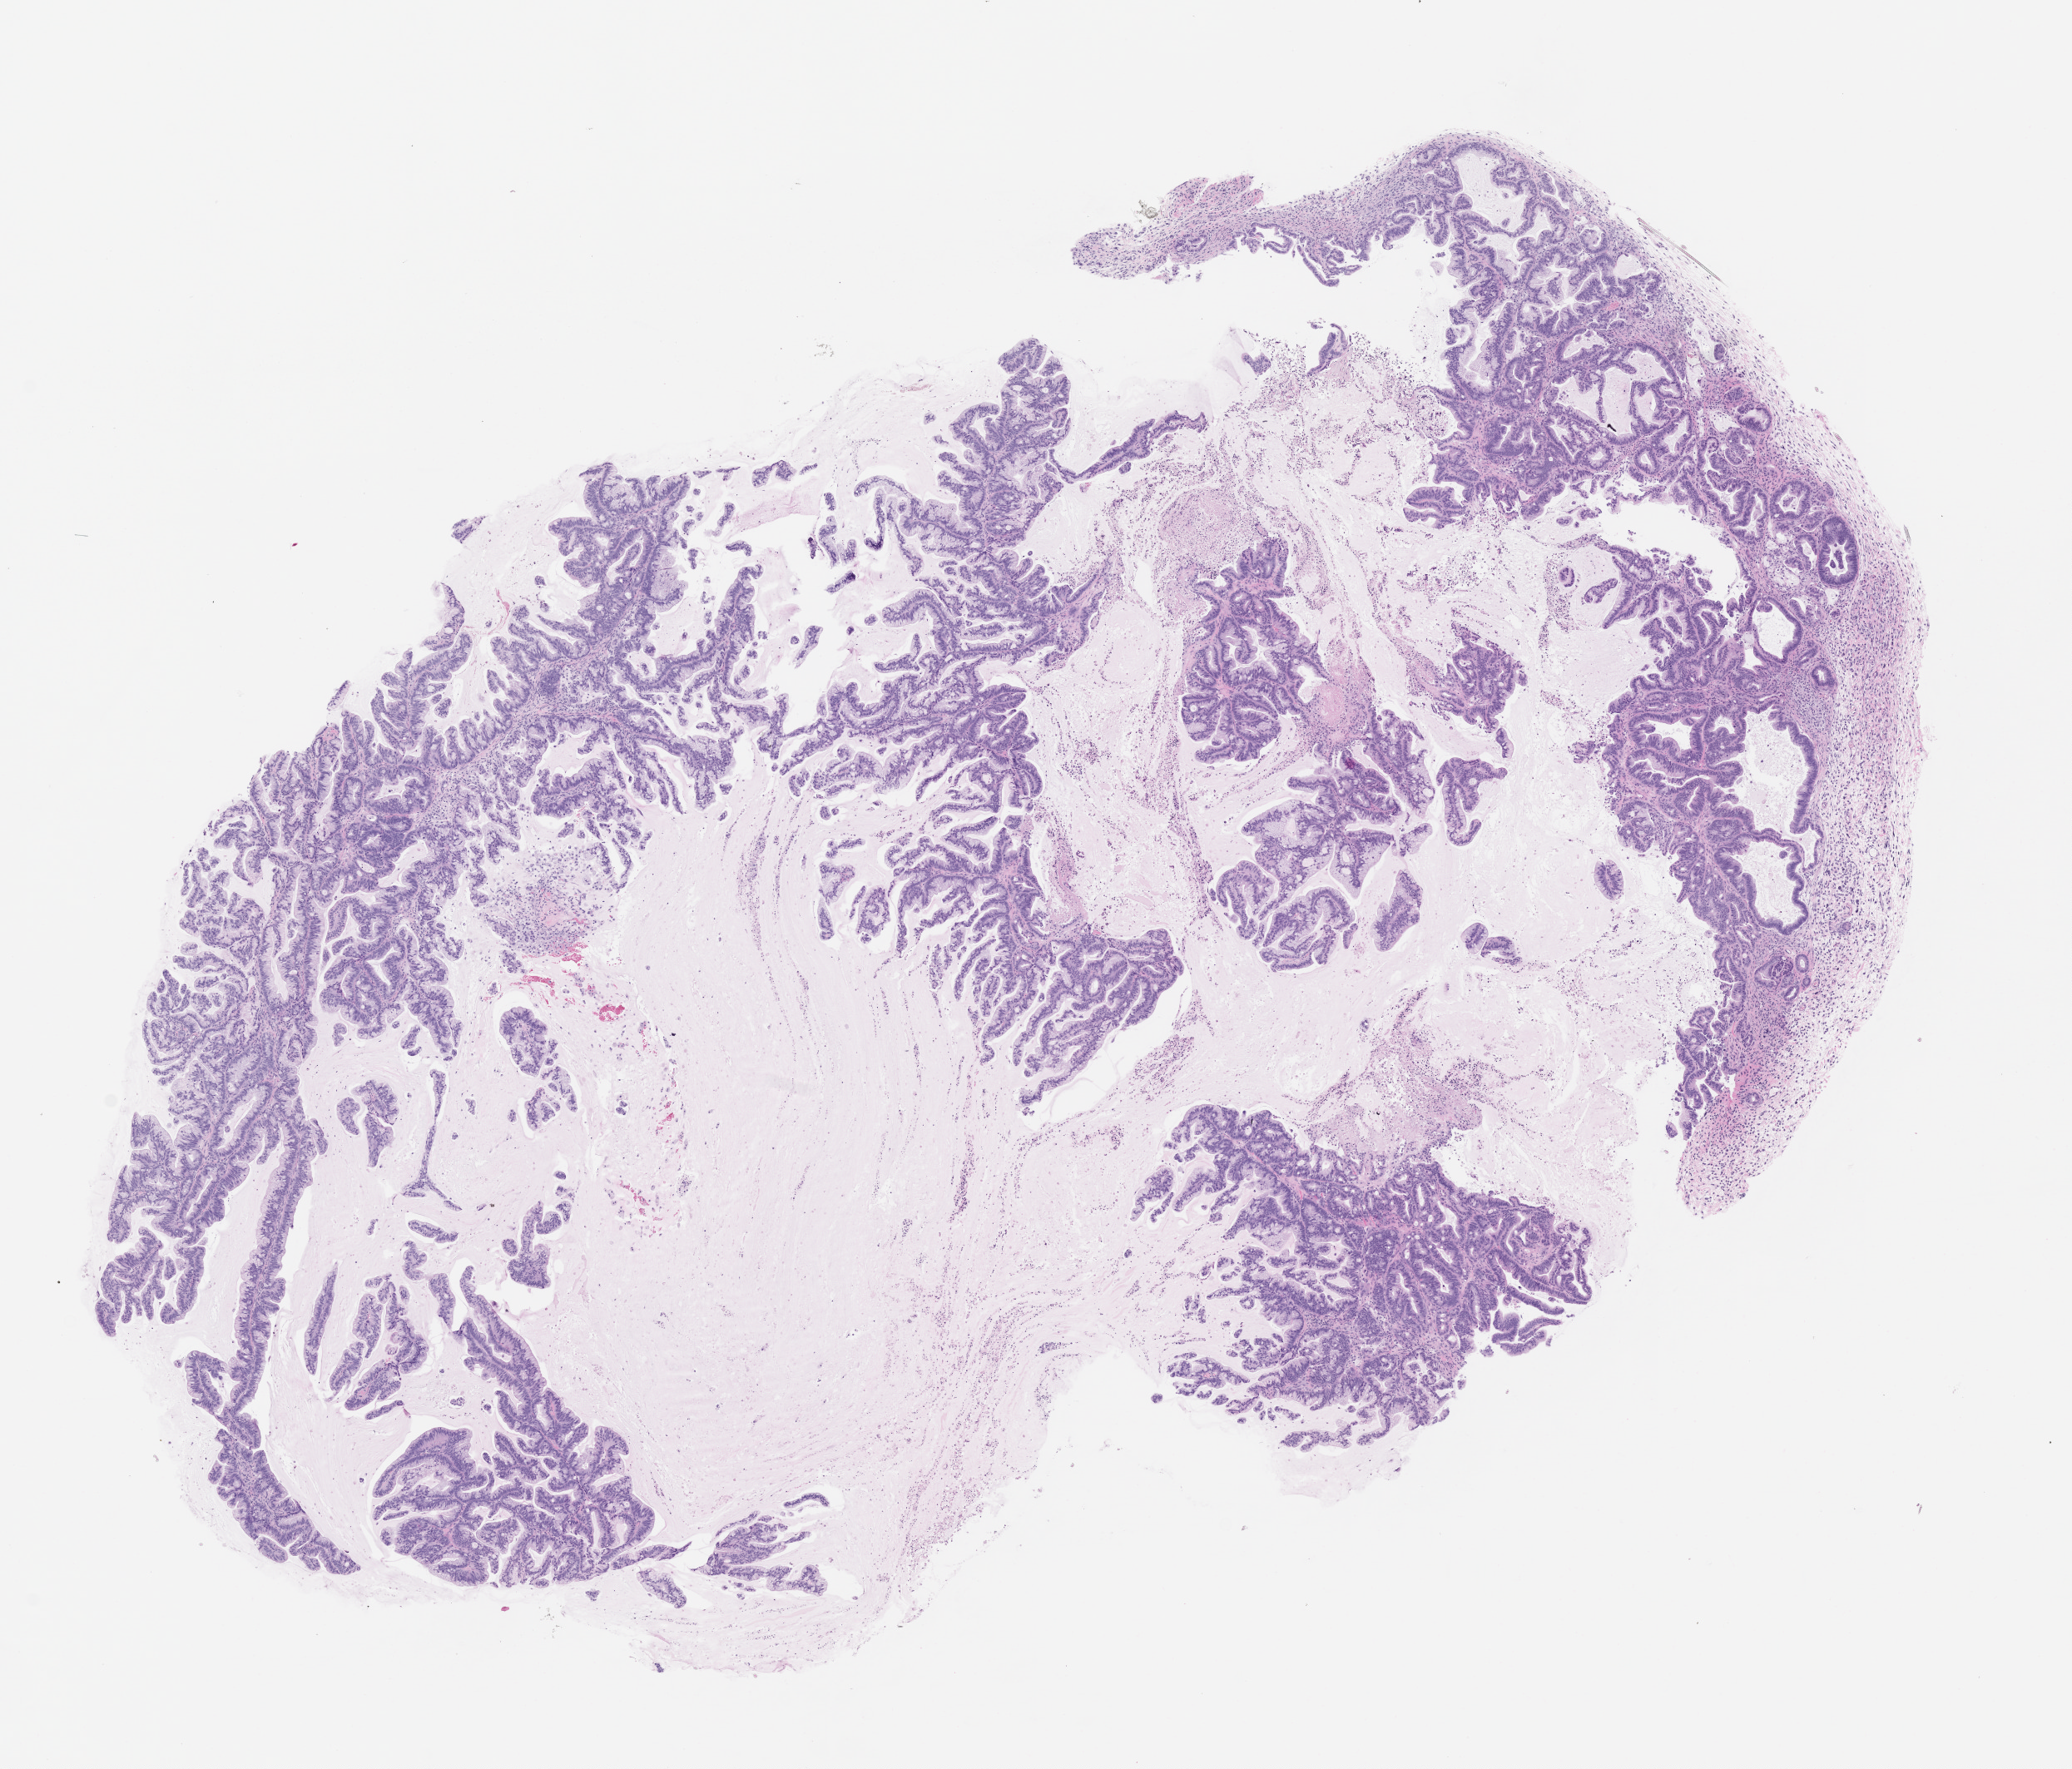
H&E whole-slide image of a patient-derived xenograft (PDX) tumor grown in a mouse, passage 1 — shown as a low-resolution overview of the whole scanned area (about 10.0 x 8.5 mm). FFPE section. Tumor site category: pancreas.
Originating patient diagnosis: Pancreatic Adenocarcinoma.